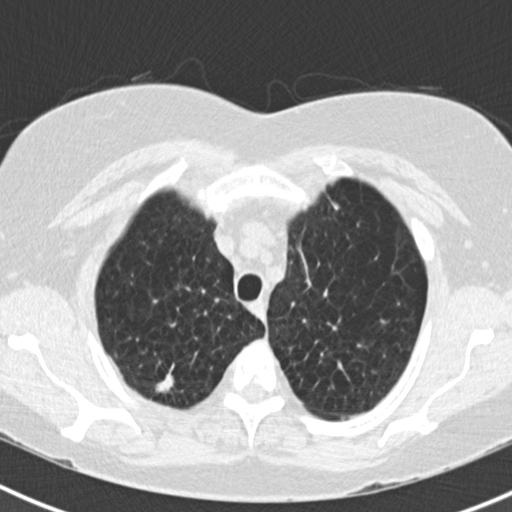
Low-dose screening chest CT, one axial slice; reconstruction kernel B30f; 120 kVp; lung window (W 1500 / L -600 HU); 2 mm slice thickness; 512 × 512 image matrix, field of view 310 × 310 mm.
Outlined on this slice (outlined manually by an expert reader):
- lesion 1 (tumor, upper lobe of right lung): bounding box <156,373,174,392> (left, top, right, bottom; pixels)